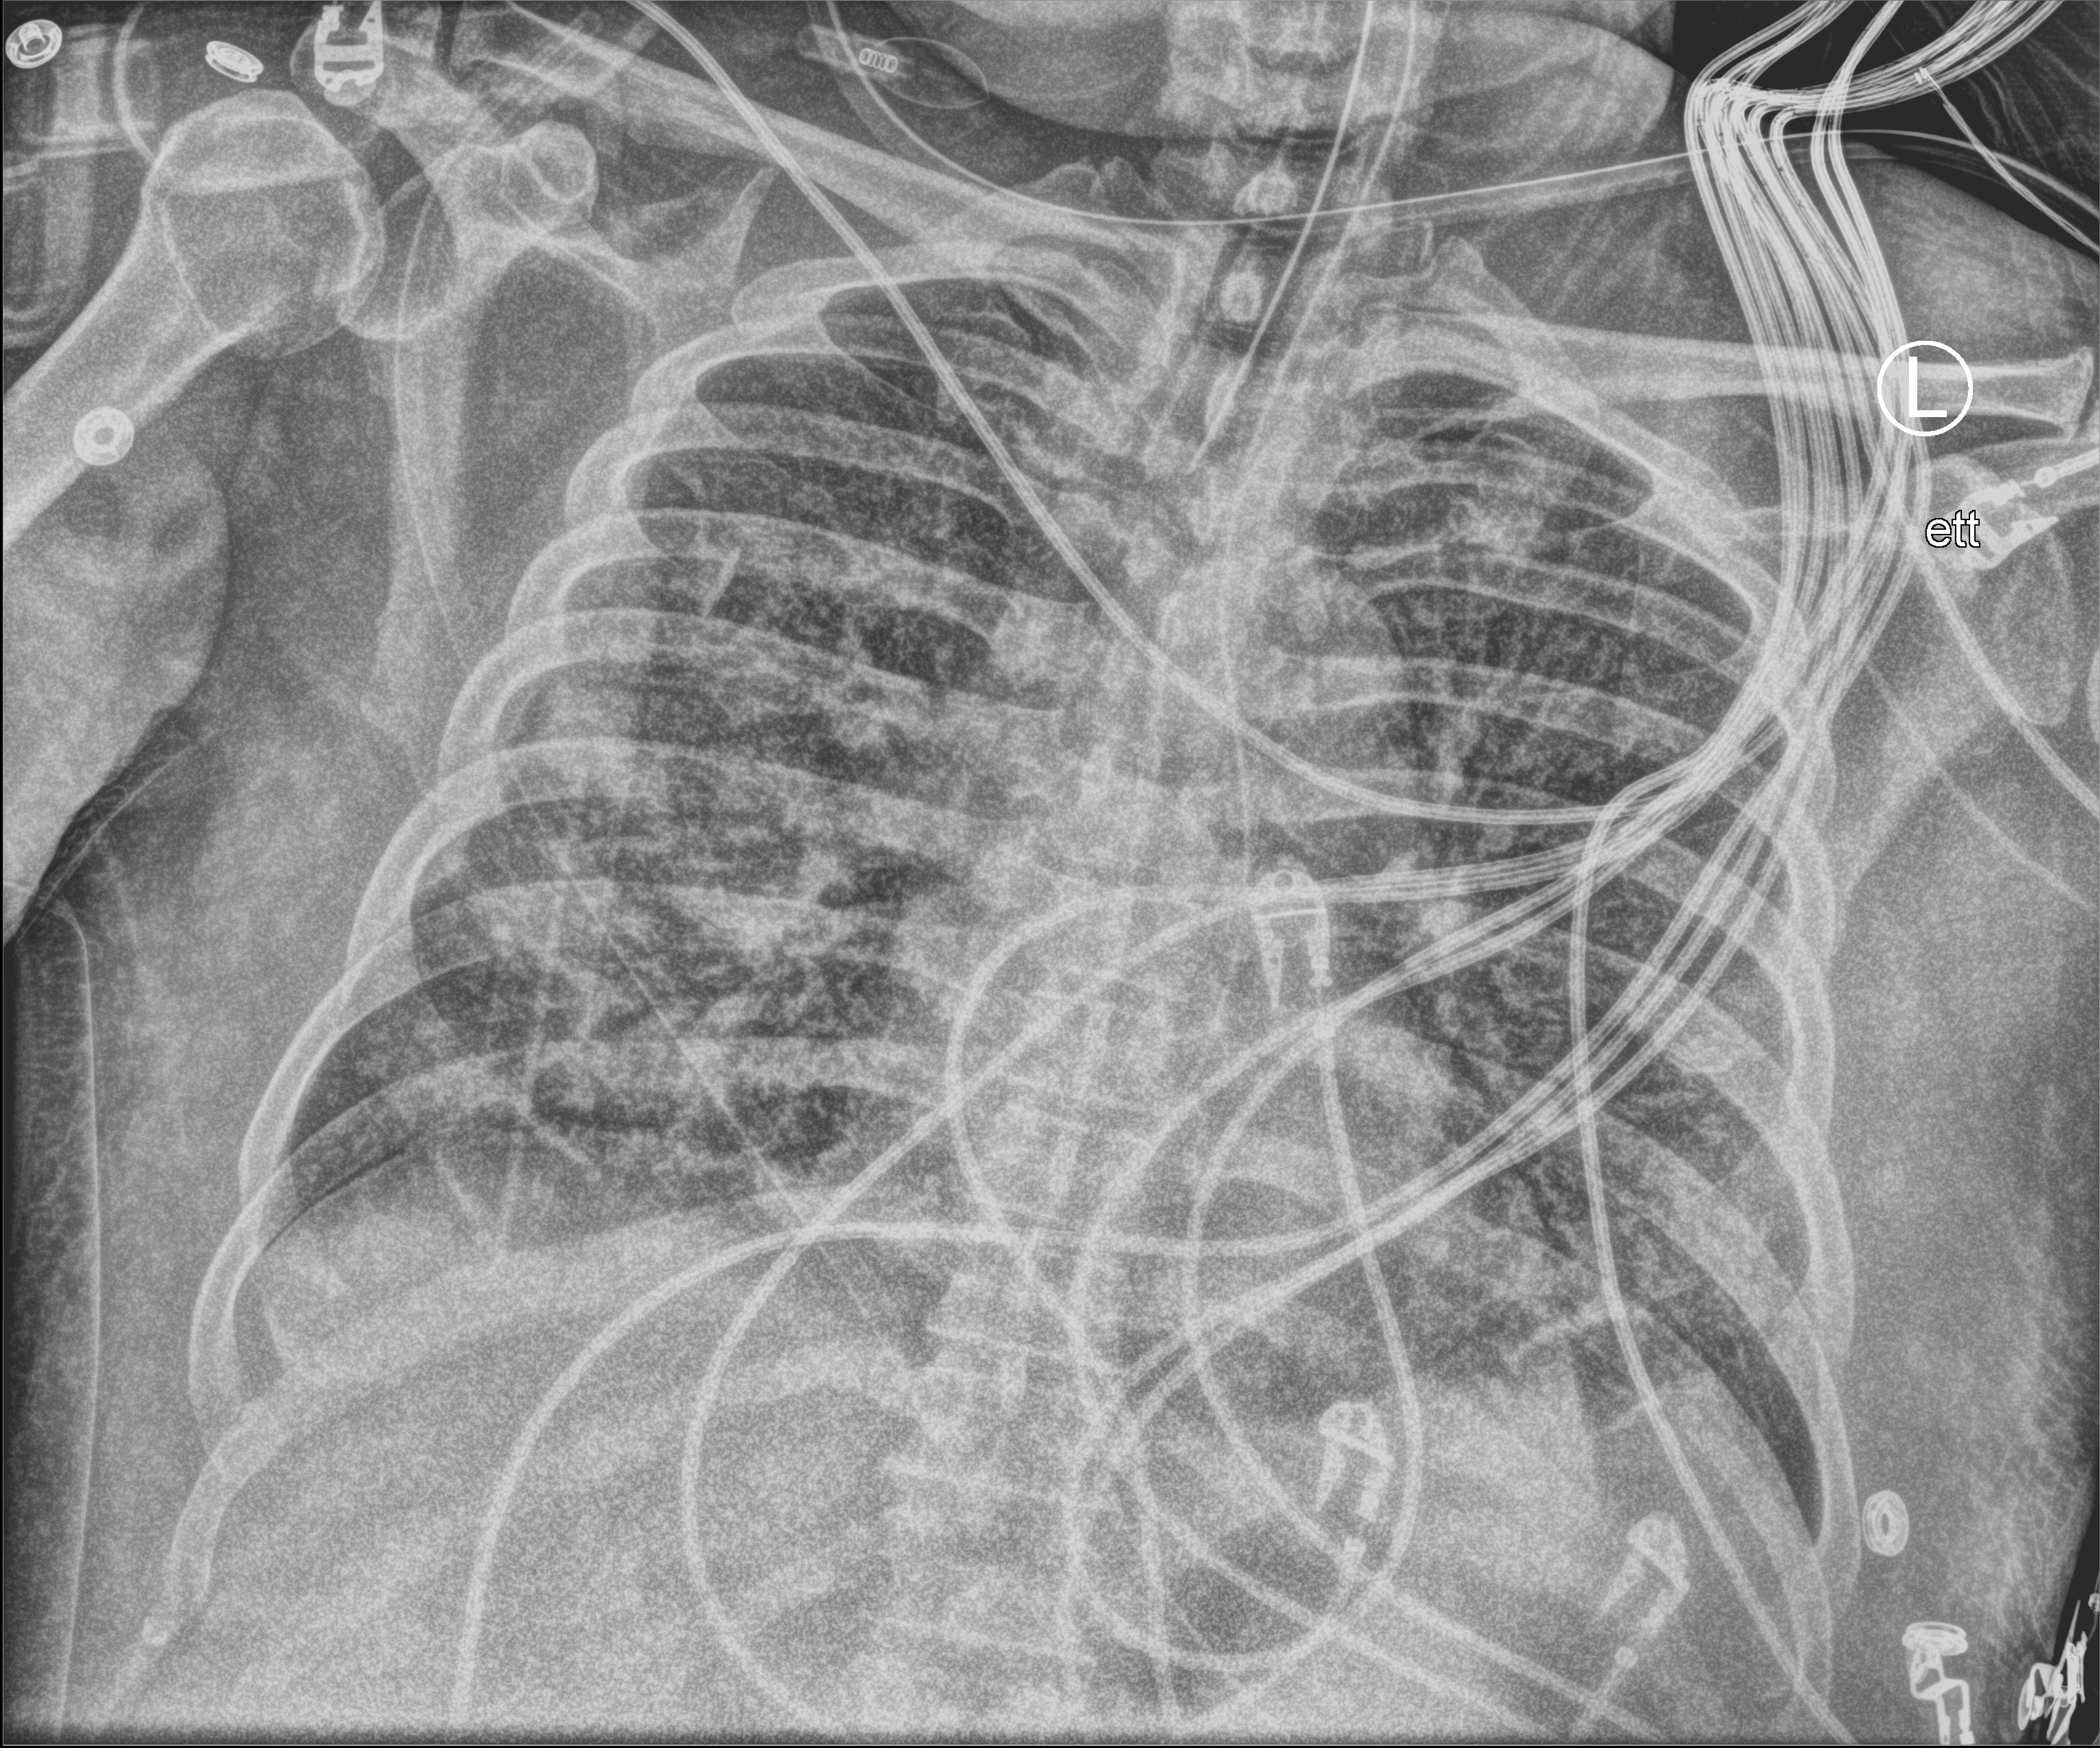
Bedside chest radiograph (computed radiography), anteroposterior (AP) projection. Patient hospitalised with COVID-19; male, aged 60–74 years.
From the hospital-stay record, not from the radiograph (when in the stay this image was taken is not recorded):
- other chronic lung disease (admission record): no
- admitted to intensive care during this hospital stay: yes